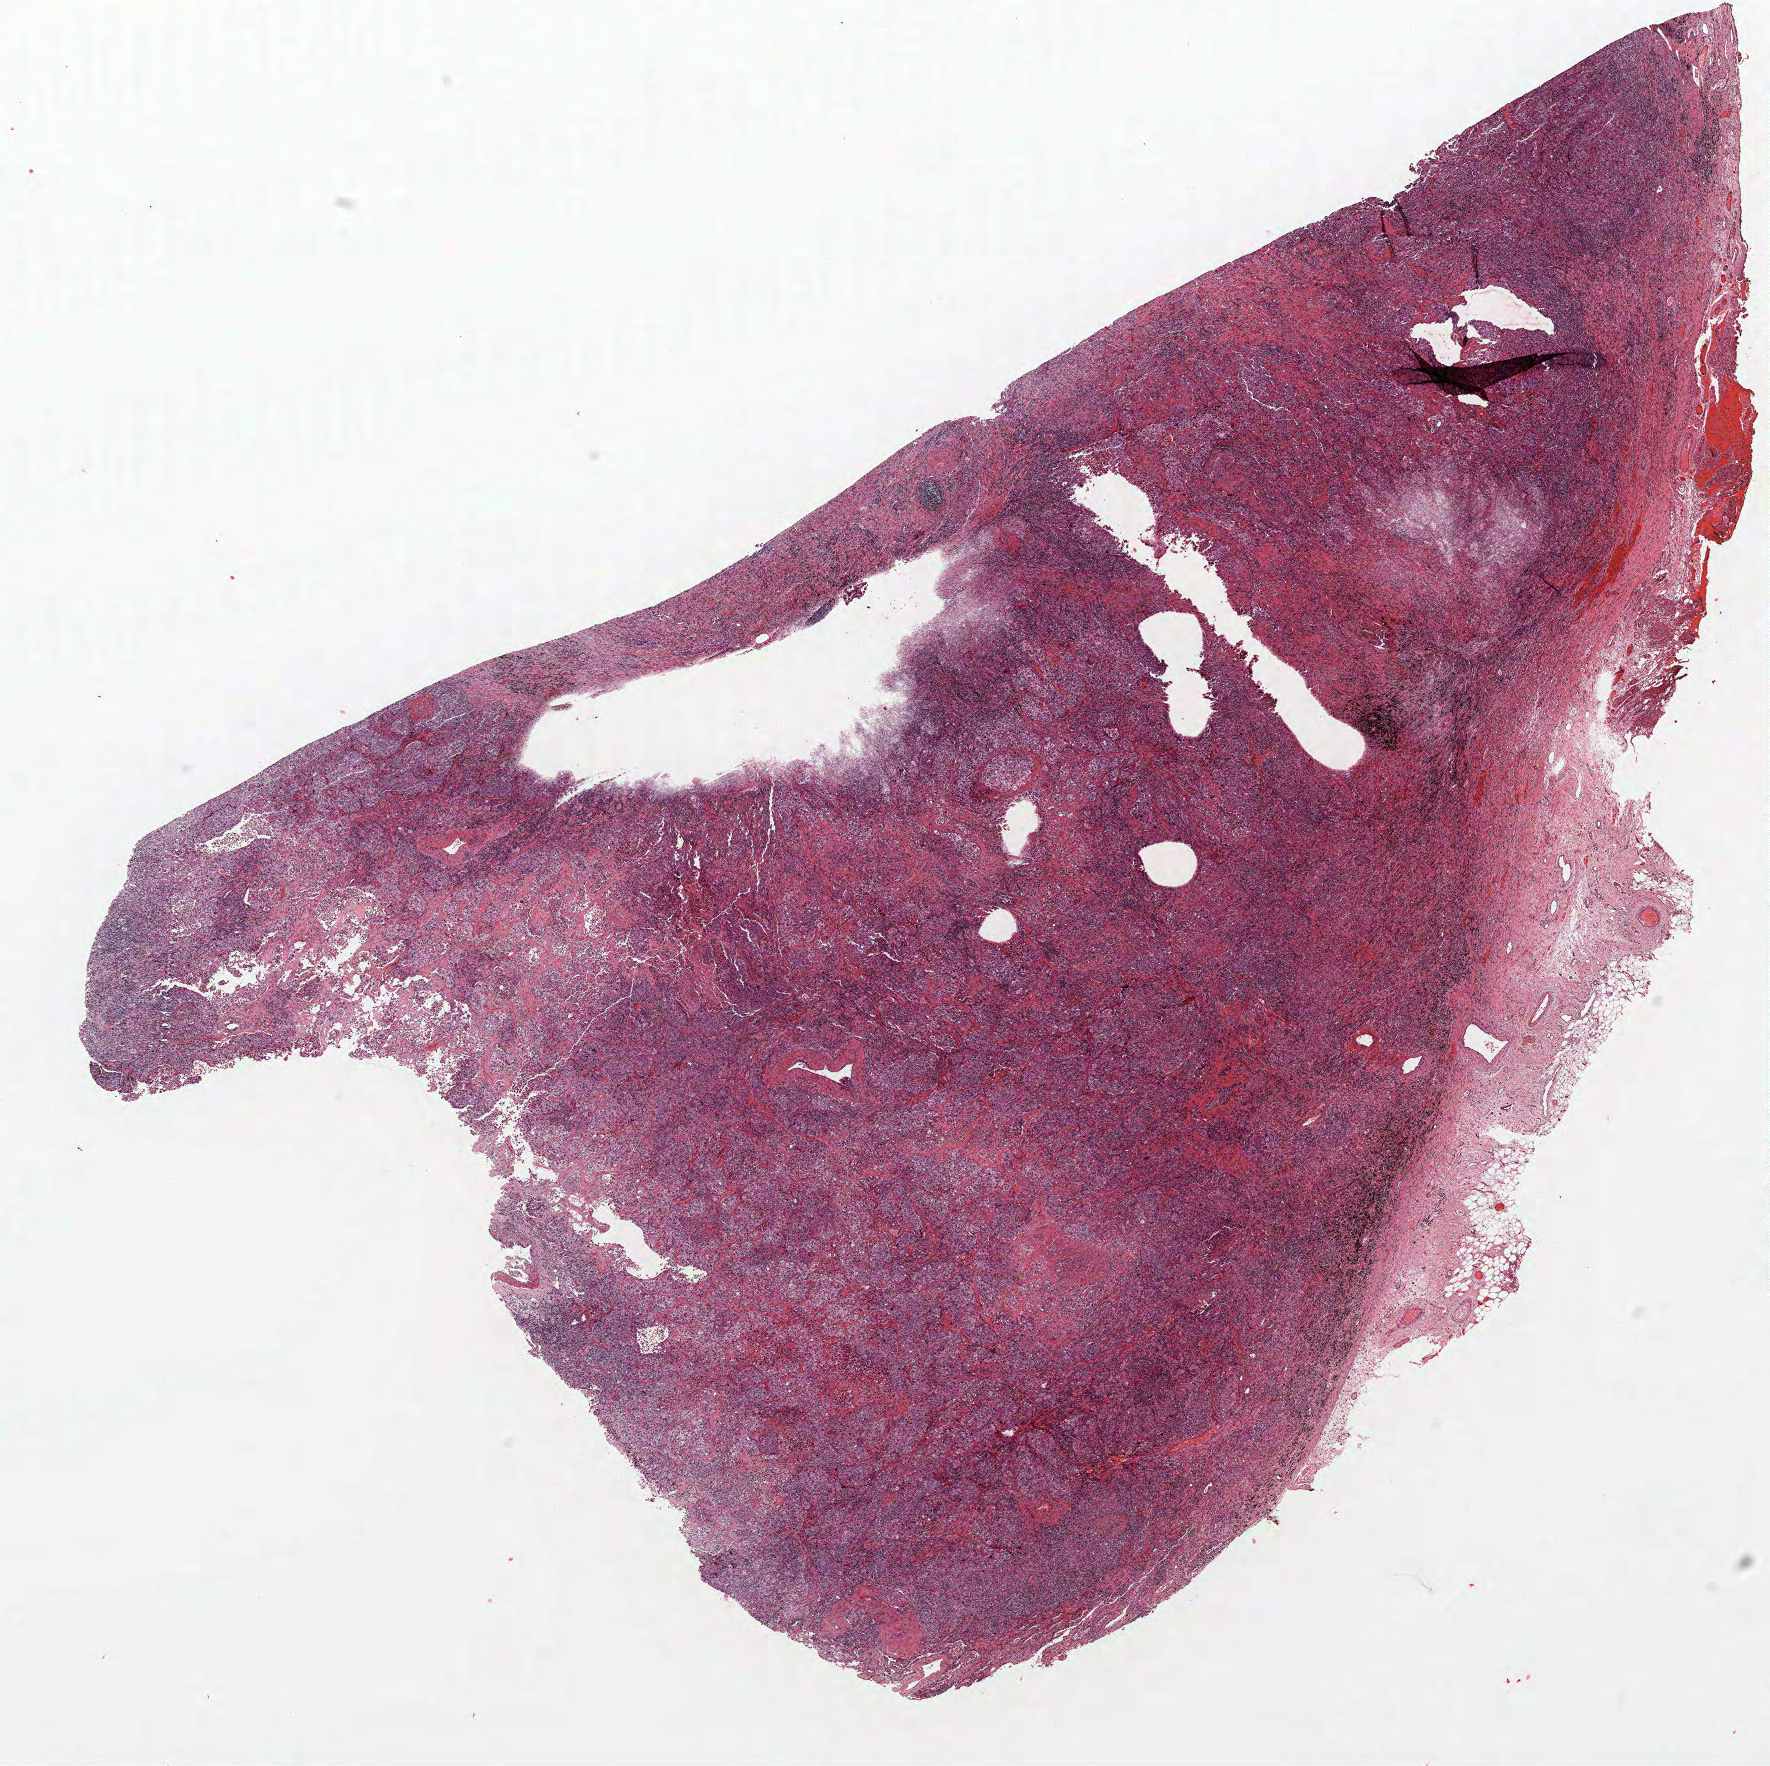
Whole-slide histology image, H&E — whole scanned area (about 14.2 x 14.1 mm) shown as a low-resolution overview; FFPE section; lung. Male patient, aged 73 at enrolment. Current smoker at enrolment. Grade: poorly differentiated (G3).
- participant's lung-cancer diagnosis: Adenocarcinoma, NOS (ICD-O-3 8140/3)
- stage (AJCC 6th edition): IIA
- primary tumour location (clinical record): right upper lobe
- tumour size (pathology): 30 mm
- ICD-O-3 topography: upper lobe of lung (C34.1)